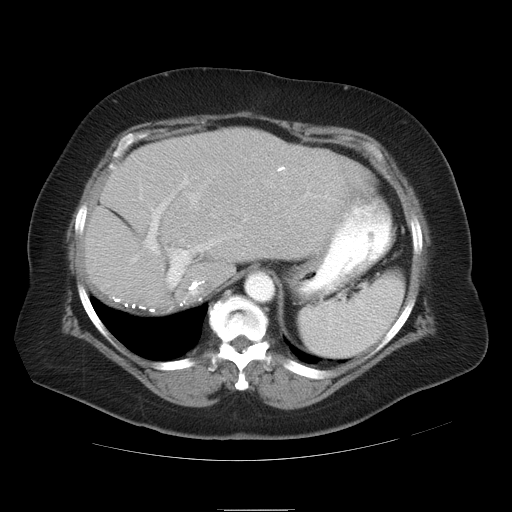
Contrast-enhanced abdominal CT, one axial slice; slice 27 of 37 in the series (ordered by position); 120 kVp; intravenous contrast given; soft-tissue window (W 400 / L 40 HU); 7.5 mm slice thickness; 512 × 512 image matrix, field of view 422 × 422 mm. Female patient, age 68 years. From the clinical record (not read from this slice): diagnosis: colorectal cancer liver metastases, imaged before liver resection; multiple liver metastases: no; largest metastasis: 2 cm; disease in both lobes: no.
Outlined on this slice (outlined manually by an expert reader):
- hepatic veins: bounding box <187,192,200,209> (left, top, right, bottom; pixels)
- liver: <85,129,374,308>
- planned liver remnant (the part of the liver to remain after resection): <92,129,374,307>
- portal vein (with intrahepatic branches): <131,174,318,304>